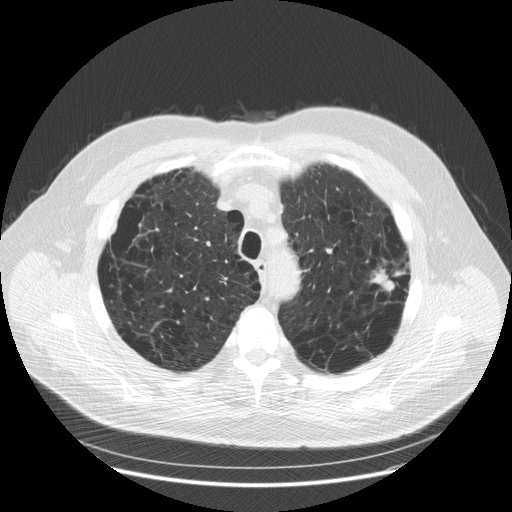
Chest CT (low-dose screening protocol), one axial image, baseline screening round, lung window (W 1500 / L -600 HU), slice 41 of 179 in the series. Male, age 70 years at enrolment. Current smoker at enrolment.
• Lesion marked by an expert reader, bounding box [x1, y1, x2, y2] px = [363, 250, 415, 300].
• Screening reader's record for this exam (one nodule recorded; not confirmed to be the boxed lesion): non-calcified nodule or mass ≥4 mm, left upper lobe, 25 × 13 mm, spiculated (stellate) margins, soft tissue attenuation.
• Official screen result: positive, change unspecified: nodule(s) >= 4 mm or enlarging nodule(s), mass(es), or other non-specific abnormalities suspicious for lung cancer.
• Later outcome: lung cancer diagnosed 62 days after this screen — adenocarcinoma, NOS, left upper lobe, moderately differentiated (G2), stage IA (AJCC 6th edition), 22 mm at pathology.